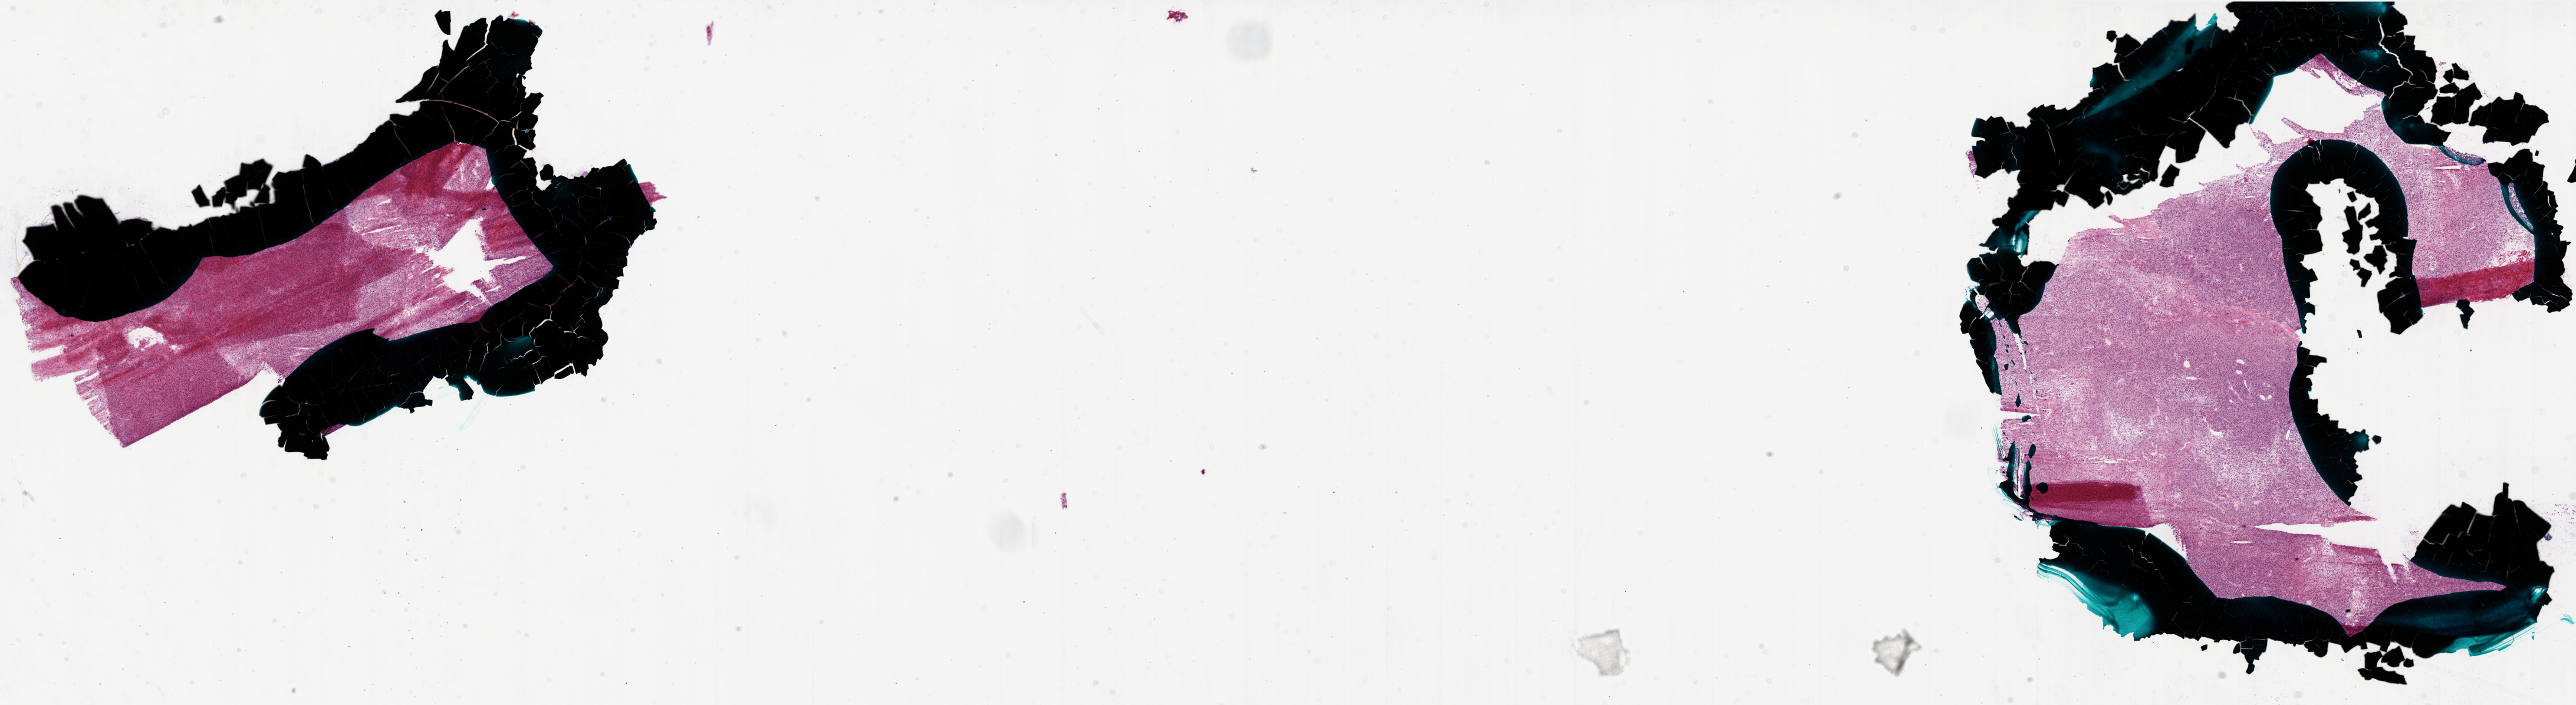
H&E whole-slide image, a low-resolution overview of the entire scanned area, about 35.0 x 9.6 mm (from a 20x scan); frozen section; sample: primary tumour, brain. Patient: male, age at initial diagnosis 76 years. Composition of this section per pathologist review: tumour cells 80%, tumour nuclei 100%.
Histologic diagnosis: Glioblastoma.